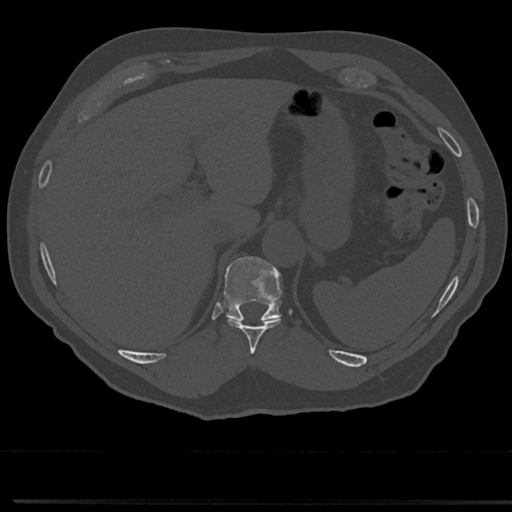
CT including the spine, one axial slice; slice 232 of 817 in the series (ordered by position); 120 kVp; bone window (W 1800 / L 400 HU); 512 × 512 image matrix, field of view 355 × 355 mm. Patient: male, 61 years. From the clinical record (not read from this slice): primary cancer: prostate.
Annotated regions visible in this slice (semi-automatically segmented with operator editing):
- T10 vertebra: bounding box <226,317,282,353> (left, top, right, bottom; pixels)
- T11 vertebra: <224,257,281,322>